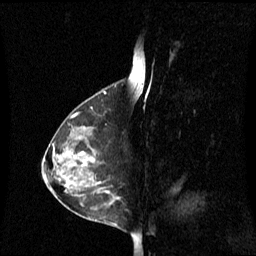
Breast MRI (dynamic contrast-enhanced), one sagittal slice. Position 33 of 60 along the scan axis. Dynamic contrast-enhanced series, image 2 of 3 at this slice position (ordered by acquisition). 1.5 T. TE 4.2 ms, TR 8.4 ms. 256 × 256 image matrix, field of view 240 × 240 mm. Female patient, age 42 years. From the clinical record (not read from this slice): setting: breast cancer imaged before/during neoadjuvant chemotherapy; receptor status: HR-positive, HER2-negative.
Structures marked on this image (semi-automatic segmentation, software-assisted and operator-edited):
- analysis volume of interest (the breast-tissue region the enhancement analysis was run in; not a lesion): bounding box (x1, y1, x2, y2) in pixels: (60, 124, 113, 195)
- tumour enhancement mask (voxels above the 70 % enhancement threshold inside the analysis volume of interest): (83, 162, 85, 165)